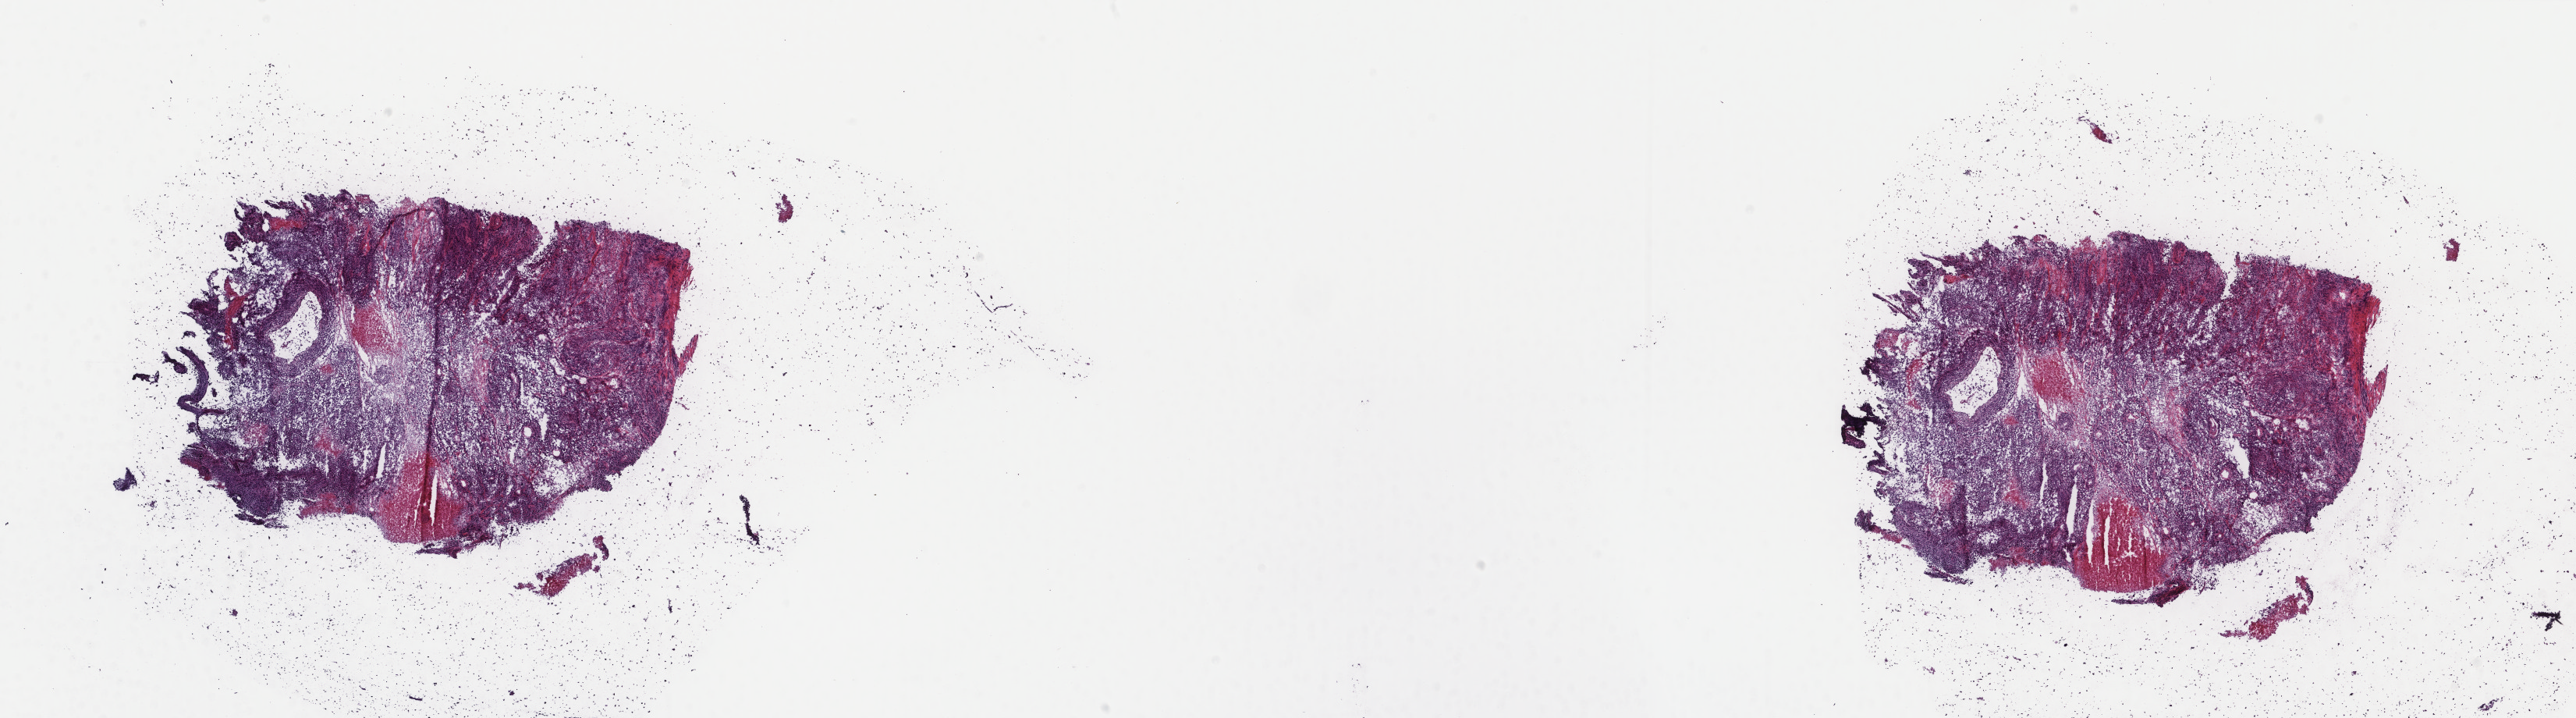
Digitized H&E-stained tissue section (whole slide) — shown as a low-resolution overview of the whole scanned area (about 26.2 x 7.3 mm). Frozen section from the top of the tissue portion. Metastatic tumour sample, sampled site: skin of trunk. Female patient; age at initial diagnosis 48 years. Slide review estimates, as recorded: tumour cells 90%, tumour nuclei 85%, normal cells 0%, stromal cells 0%, necrosis 10%. Infiltration values recorded for this section: lymphocyte infiltration 0%, monocyte infiltration 0%, neutrophil infiltration 0%.
This section: metastatic tumour tissue. Patient diagnosis: Malignant melanoma, NOS.